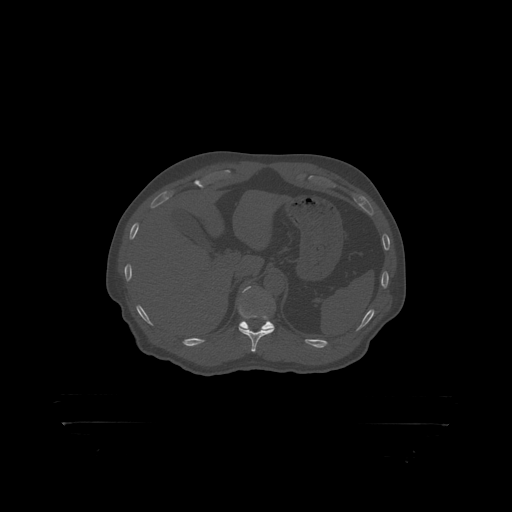
CT including the spine, one axial slice. Position 369 of 399 along the scan axis. 120 kVp. Bone window (W 1800 / L 400 HU). 512 × 512 image matrix, field of view 650 × 650 mm. Male patient, age 46 years. From the clinical record (not read from this slice): primary cancer: skin.
Annotated regions visible in this slice (semi-automatically segmented with operator editing):
- T11 vertebra: bounding box [x1, y1, x2, y2] px = [239, 307, 267, 318]
- T12 vertebra: [243, 287, 270, 318]